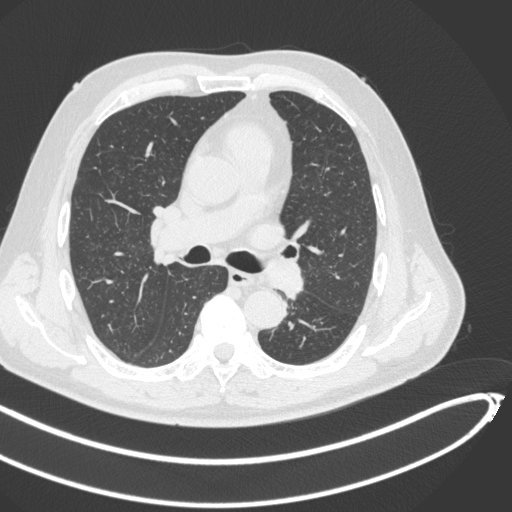
Chest CT, one axial slice; slice 275 of 466 in the series (ordered by position); 120 kVp; lung window (W 1500 / L -600 HU); 512 × 512 image matrix. Male patient, age 64 years. Case-level facts recorded for this patient, not image findings: clinical TNM (as recorded): T1c N0 M0; histopathological grade: G2.
Annotated regions visible in this slice (bounding box drawn by a radiologist):
- lung tumour (recorded histology: squamous cell carcinoma): bounding box <267,257,306,300> (left, top, right, bottom; pixels)